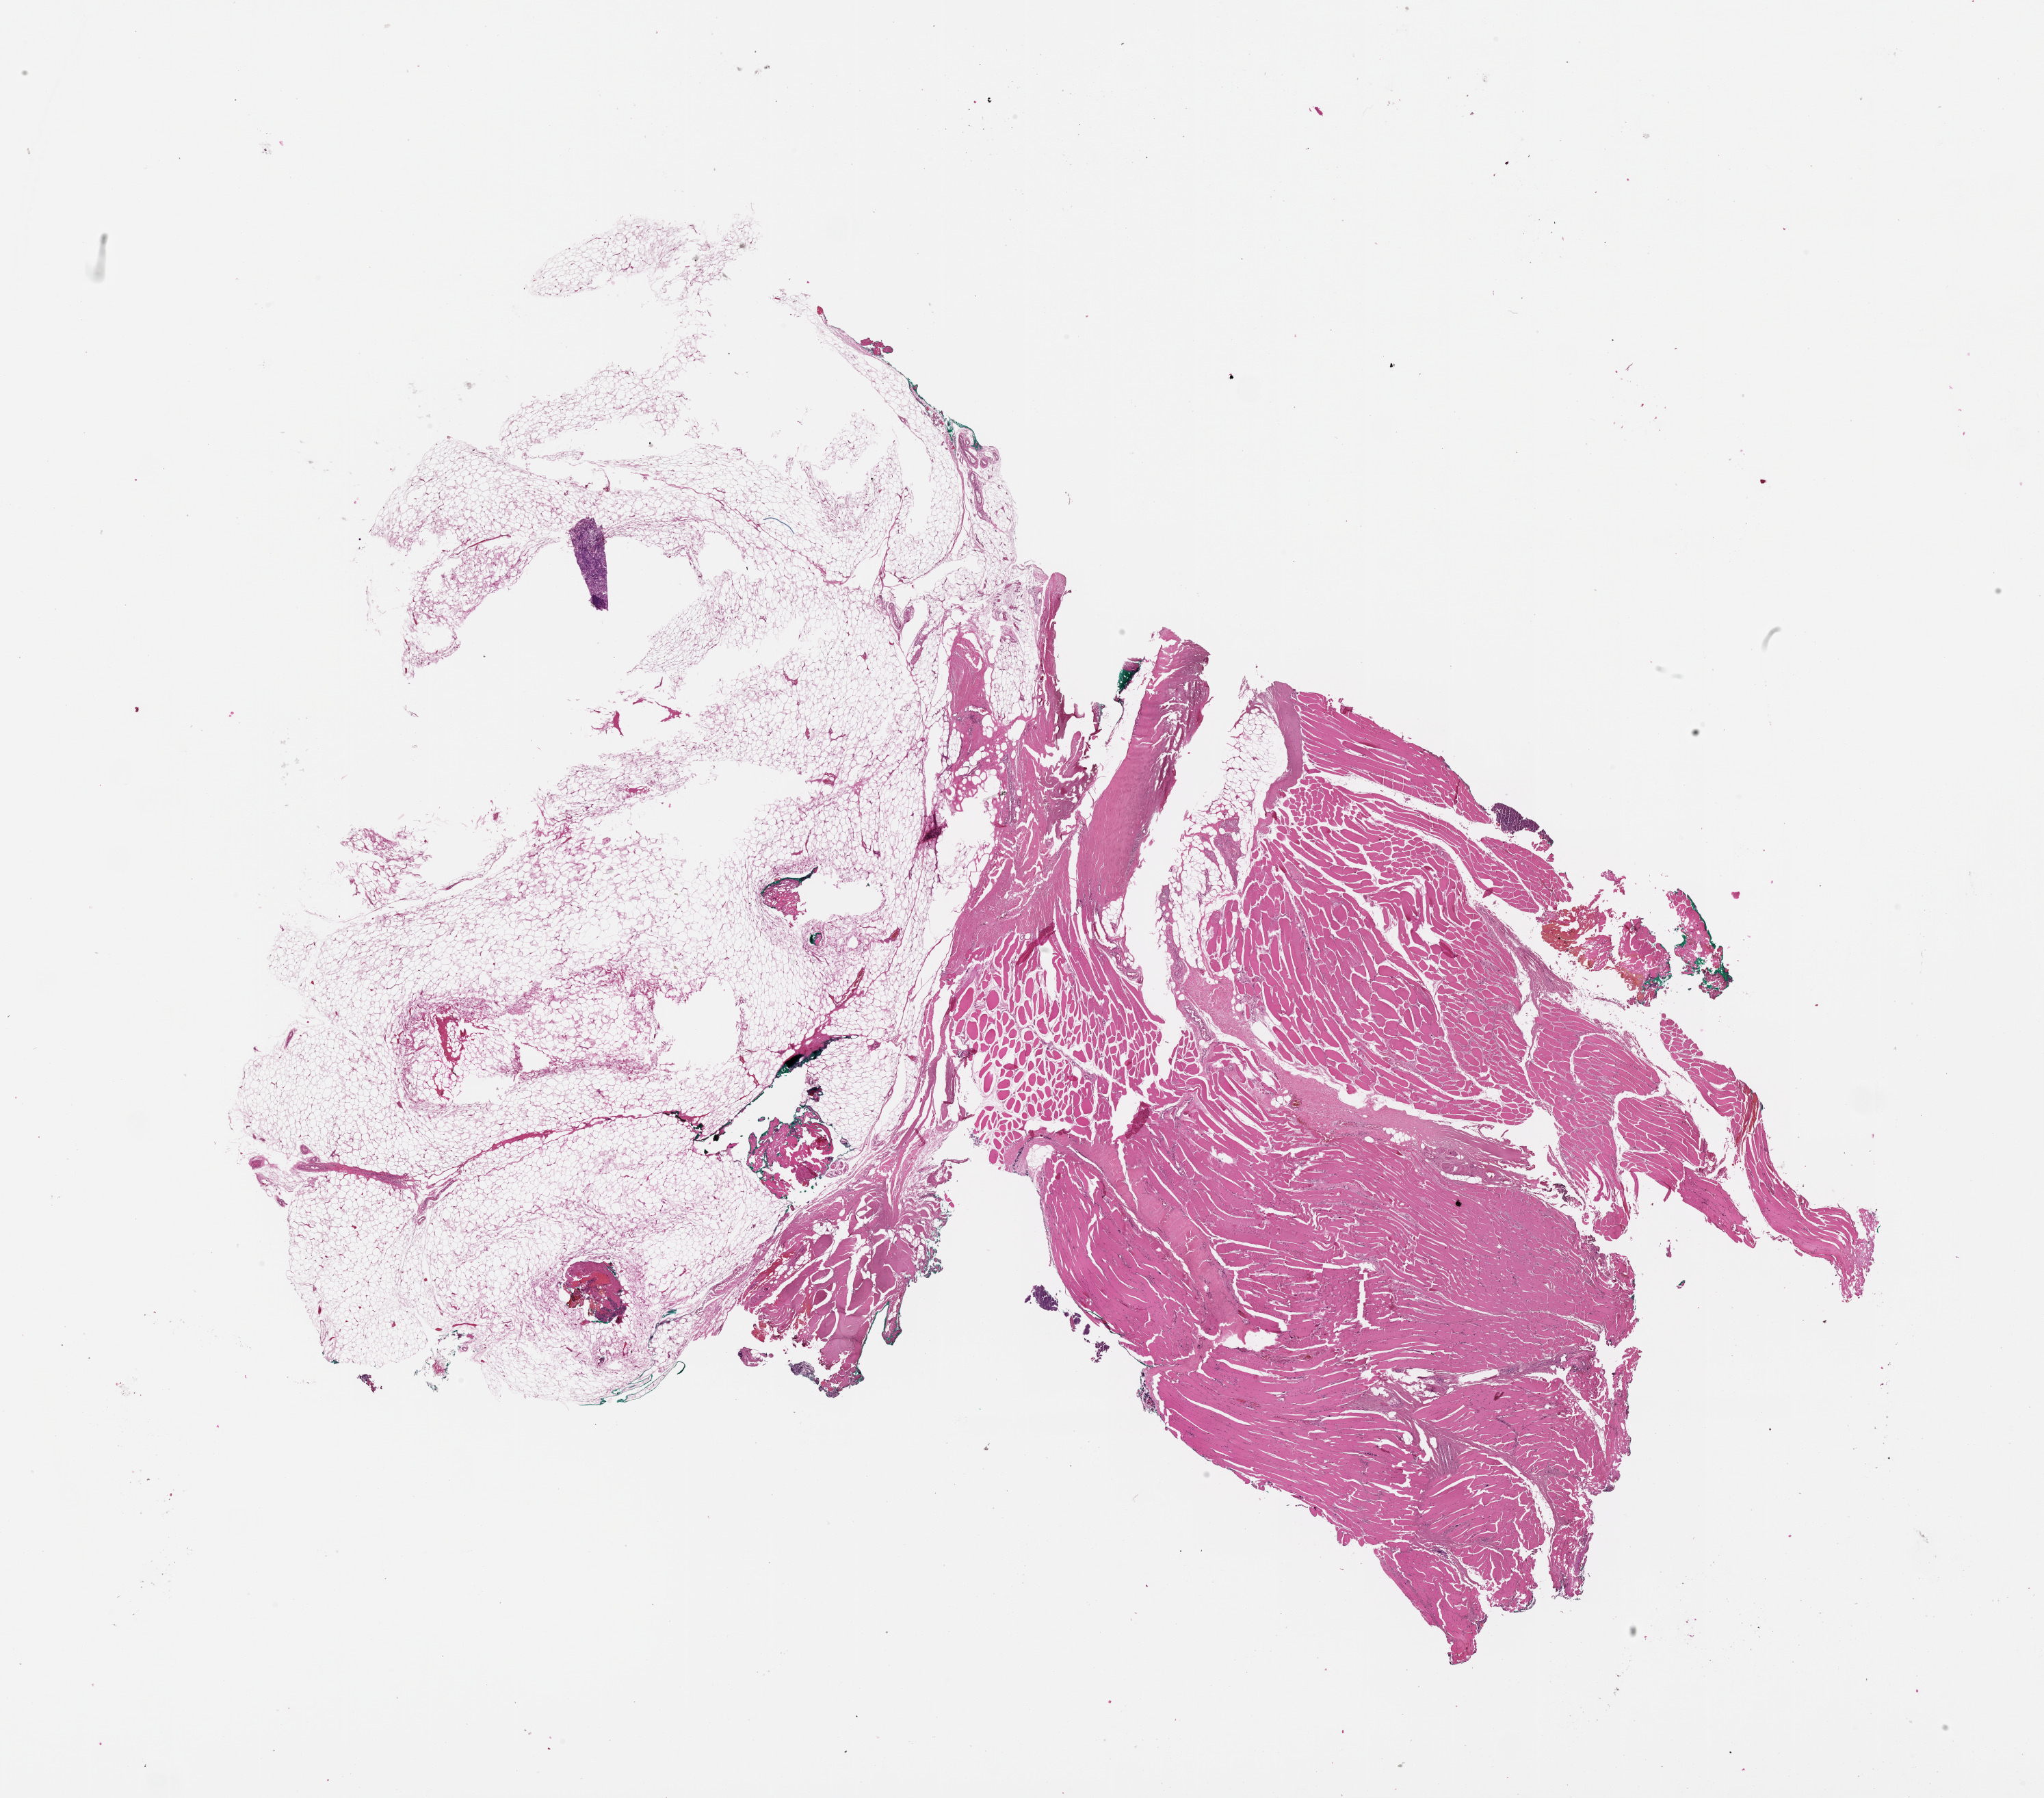
H&E whole-slide image — low-resolution overview of the scanned area, about 24.1 x 21.2 mm.
Patient diagnosis (cohort enrolment): sarcoma (site not recorded at cohort level).